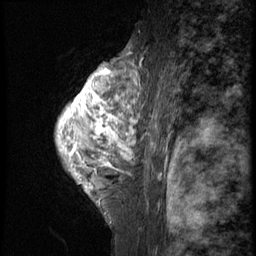
Breast MRI (dynamic contrast-enhanced), one sagittal slice. Position 43 of 58 along the scan axis. 3 images stored at this slice position (order not interpretable as contrast timing). 1.5 T. TE 4.2 ms, TR 9 ms. 2.5 mm slice thickness. 256 × 256 image matrix, field of view 180 × 180 mm. Female patient, age 50 years. Case-level facts recorded for this patient, not image findings: setting: breast cancer imaged before/during neoadjuvant chemotherapy; receptor status: triple-negative.
Outlined on this slice (semi-automatically segmented with operator editing):
- analysis volume of interest (the breast-tissue region the enhancement analysis was run in; not a lesion): bounding box [x1, y1, x2, y2] px = [56, 48, 129, 214]
- tumour enhancement mask (voxels above the 140 % enhancement threshold inside the analysis volume of interest): [58, 65, 129, 192]